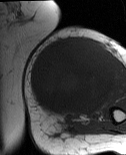
MRI of an extremity soft-tissue mass, one axial slice. Slice 29 of 86 in the series (ordered by position). MR volume resampled by the dataset authors to the PET/CT grid (not the native acquisition matrix). 3.27 mm slice thickness. 126 × 155 image matrix. Female patient. From the clinical record (not read from this slice): histological type: pleiomorphic leiomyosarcoma; grade: high; site of the primary tumour: left biceps.
Outlined on this slice (expert contour drawn on MRI and transferred to this co-registered scan by the dataset authors):
- gross tumour volume including surrounding oedema: bounding box [x1, y1, x2, y2] px = [29, 38, 115, 118]
- gross tumour volume (mass): [29, 38, 115, 118]